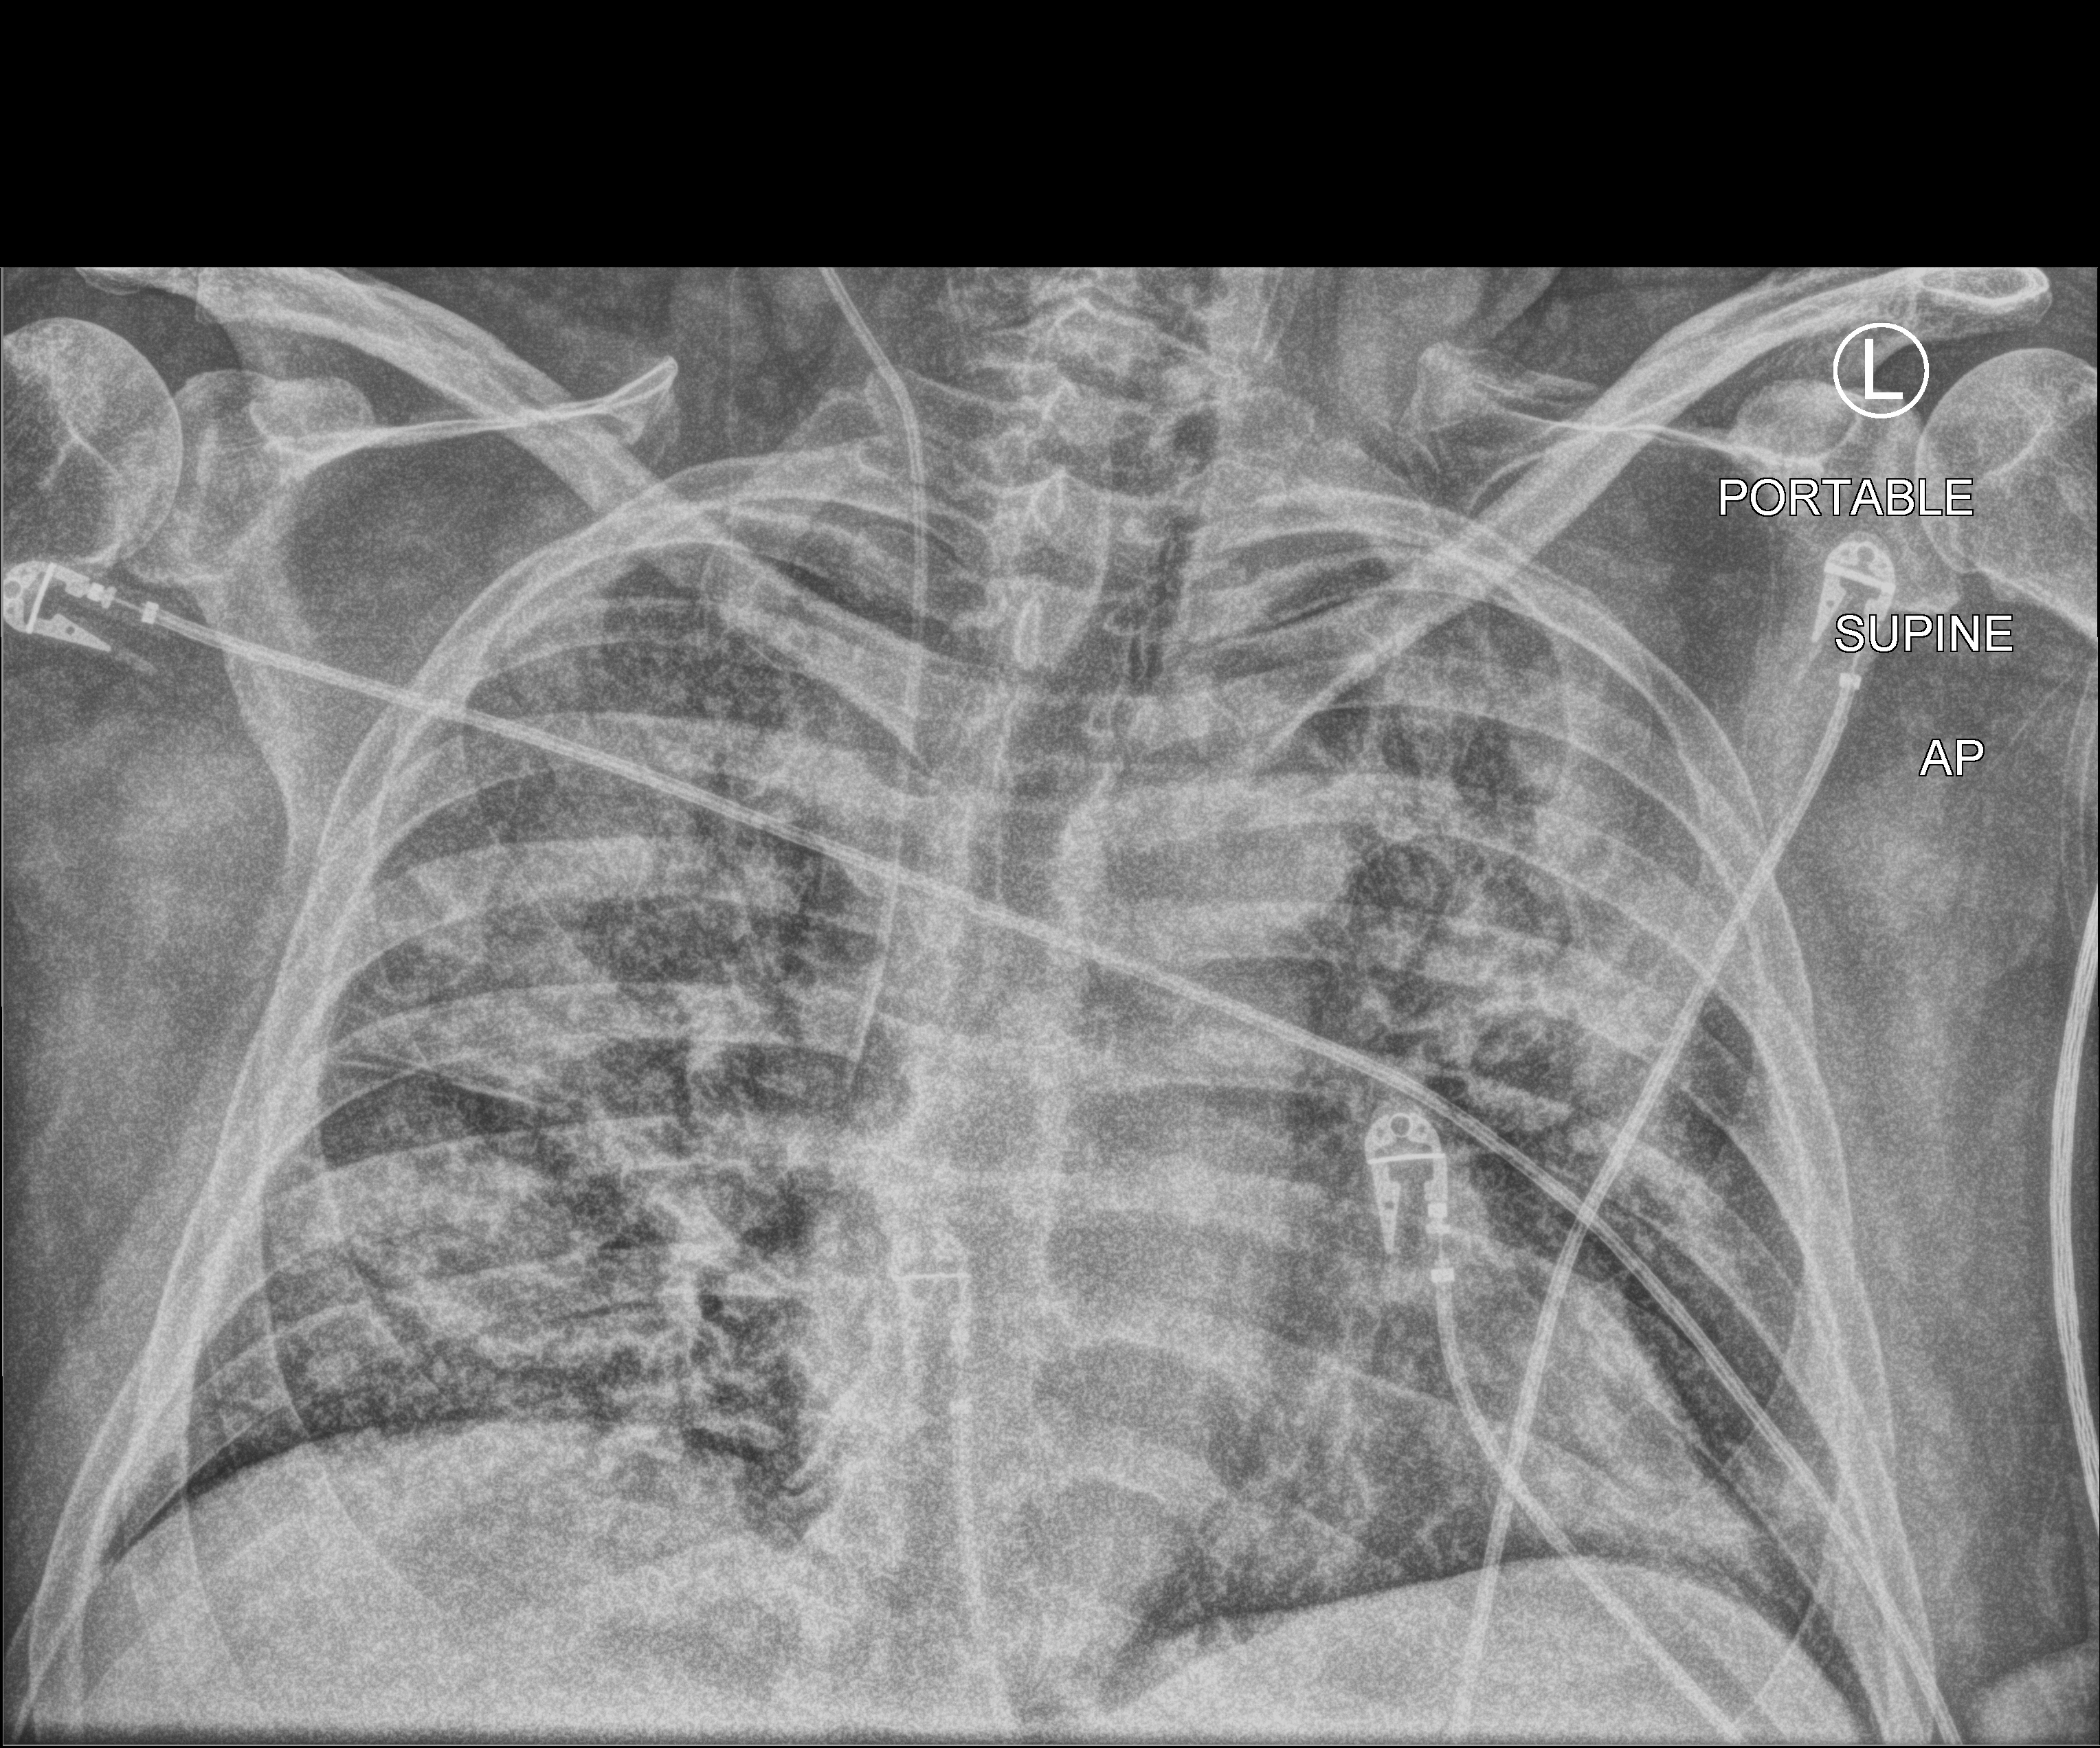
Bedside chest radiograph (computed radiography). Patient hospitalised with COVID-19; male, aged 60–74 years.
From the hospital-stay record, not from the radiograph (when in the stay this image was taken is not recorded): diabetes (admission record): no.